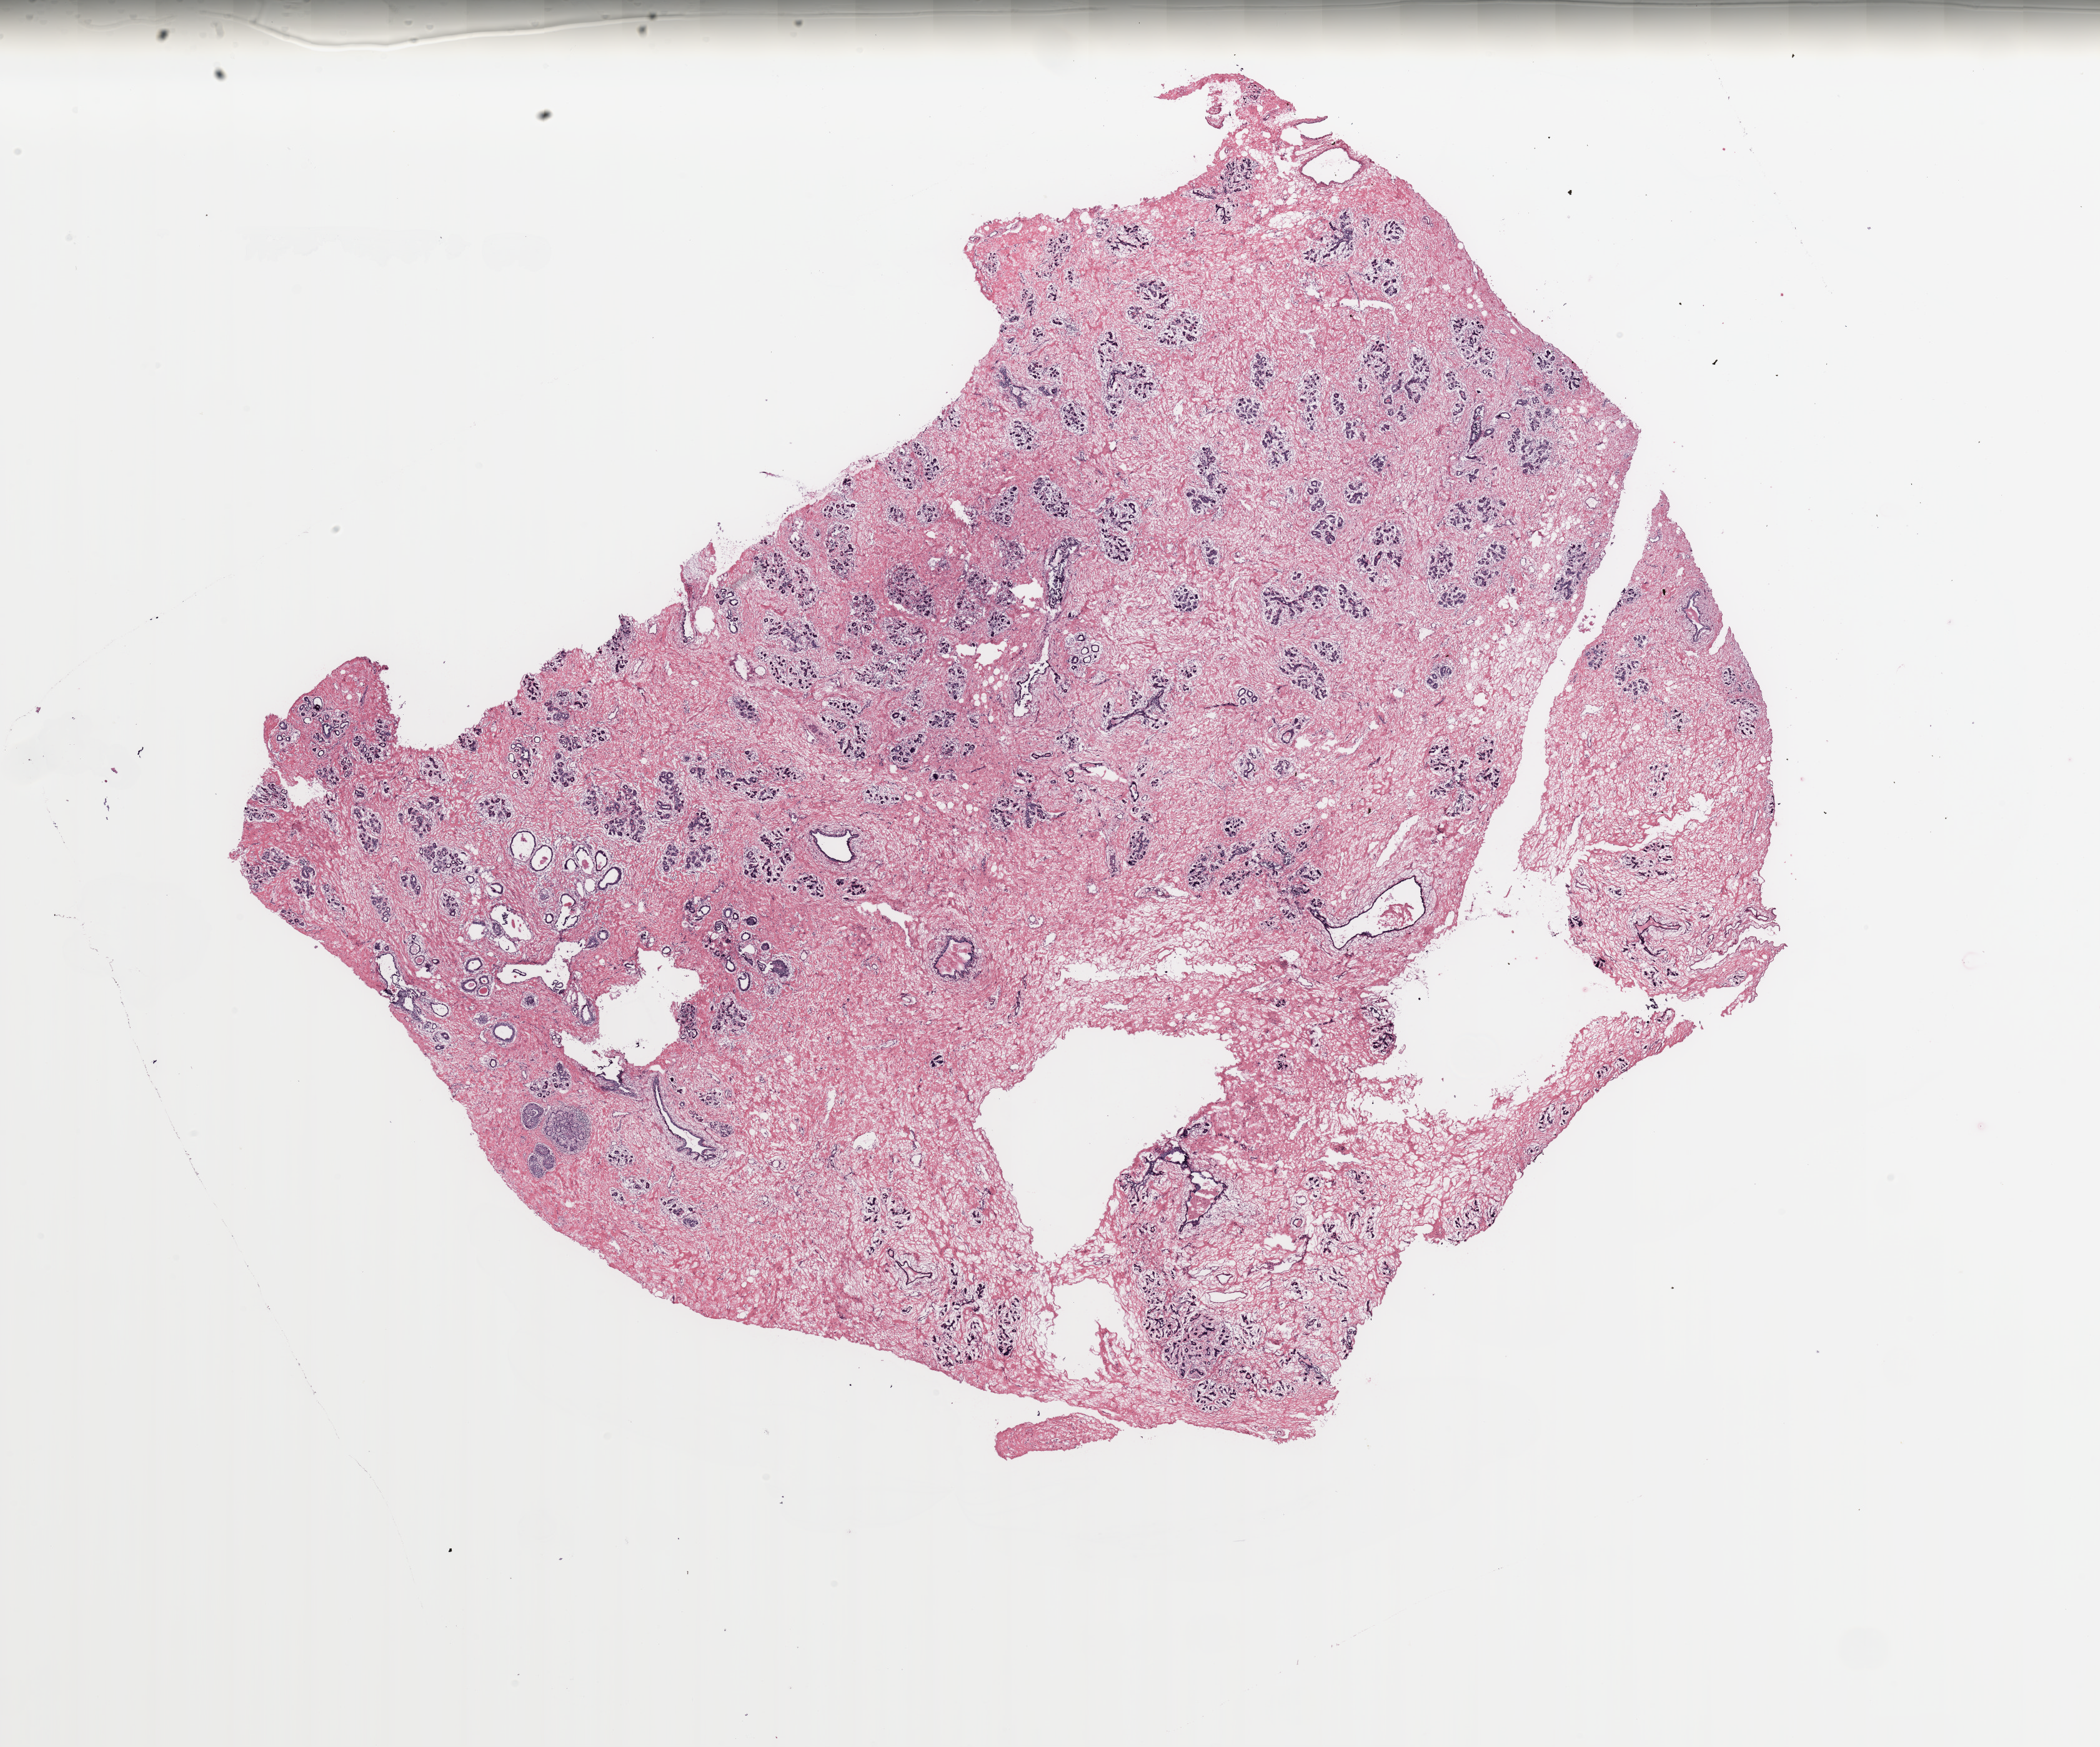
Whole-slide histology image, H&E-stained — shown as a low-resolution overview of the whole scanned area (about 26.6 x 22.1 mm, from a 20x scan). Breast, tissue type not recorded.
- patient diagnosis (cohort enrolment): breast cancer (breast)